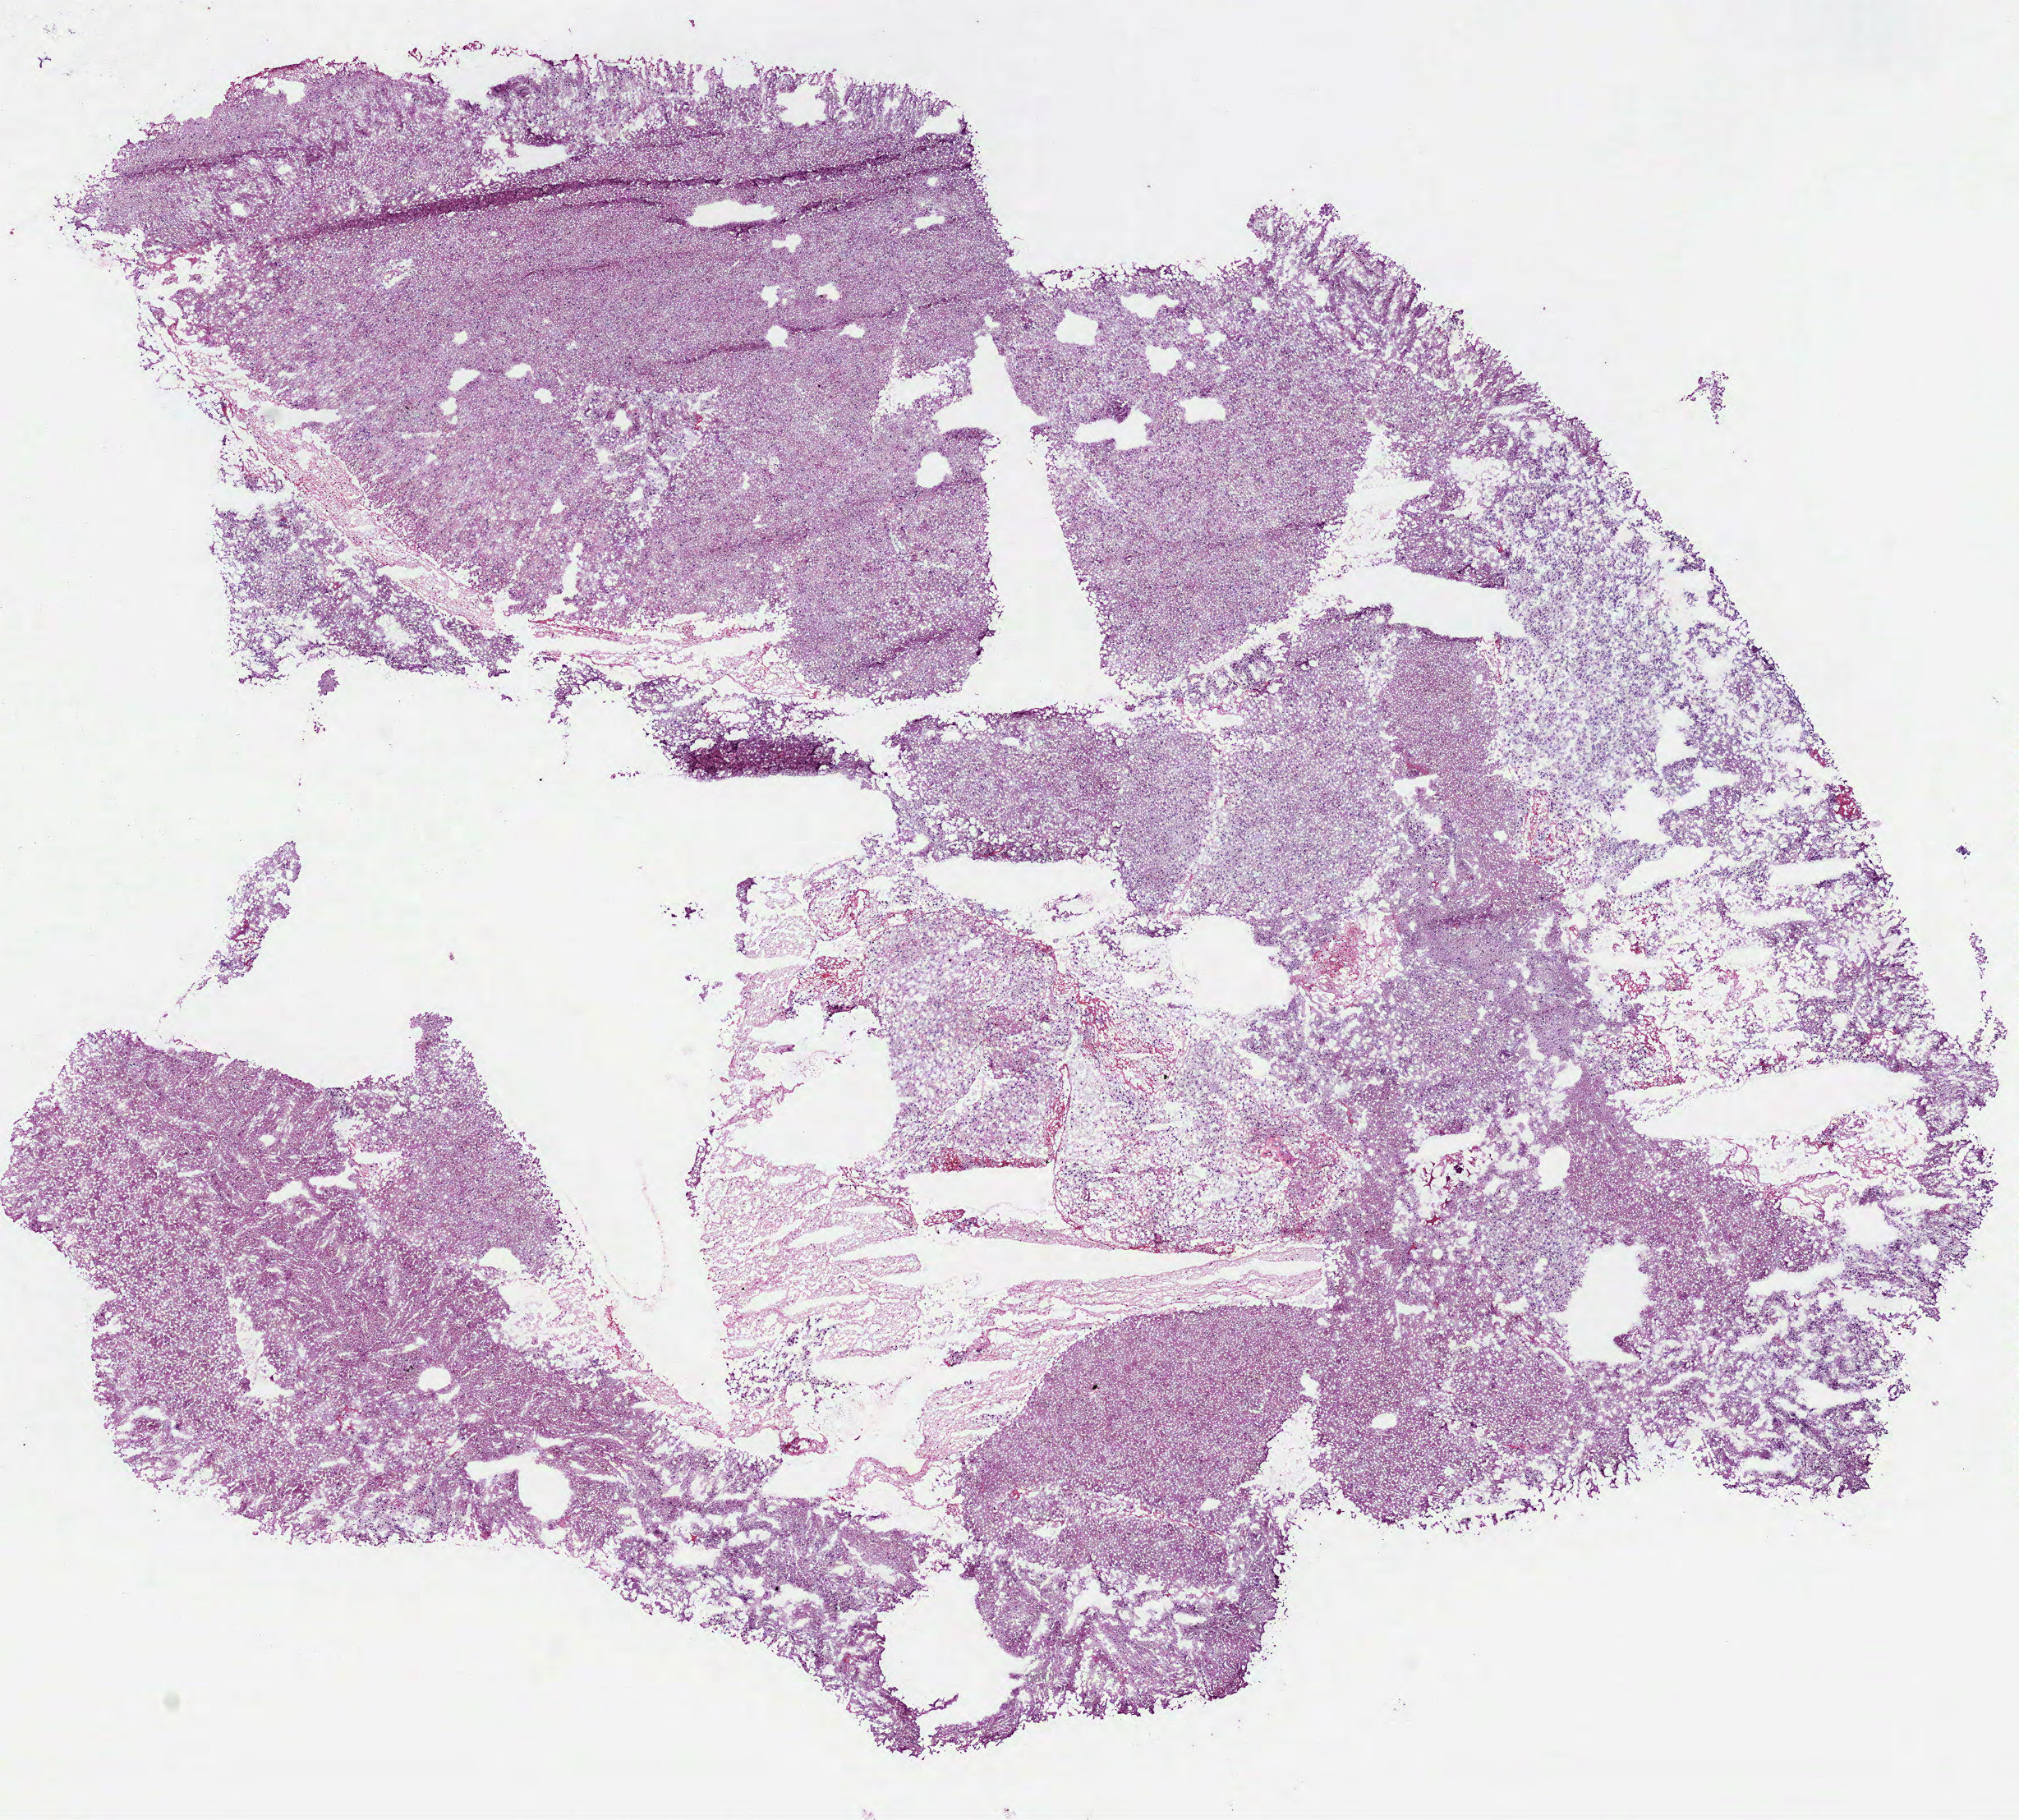
Hematoxylin and eosin (H&E) stained whole-slide image, shown as a low-resolution overview of the whole scanned area (about 9.9 x 8.9 mm, from a 40x scan), frozen section from the bottom of the tissue portion, sample: primary tumour, brain. Male patient; age at initial diagnosis 67 years. Histologic grade: G3 (poorly differentiated). Composition of this section per pathologist review: tumour cells 100%, tumour nuclei 65%, normal cells 0%, stromal cells 0%, necrosis 0%.
Histologic diagnosis: Mixed glioma. Laterality: right.